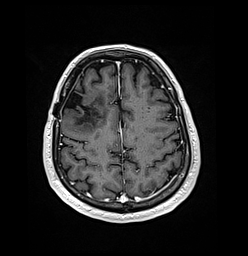
Brain MRI from a brain-tumour surgery series, one axial slice; position 46 of 176 along the scan axis; T1-weighted post-contrast; 1 mm slice thickness; 248 × 256 image matrix, field of view 242 × 250 mm. Case-level facts recorded for this patient, not image findings: histopathology: Oligodendroglioma; WHO grade: 3; IDH mutation: yes; tumour location: Right Frontal.
Annotated regions visible in this slice (manually delineated by an expert):
- previous resection cavity: box from (x=63, y=88) to (x=85, y=110) px